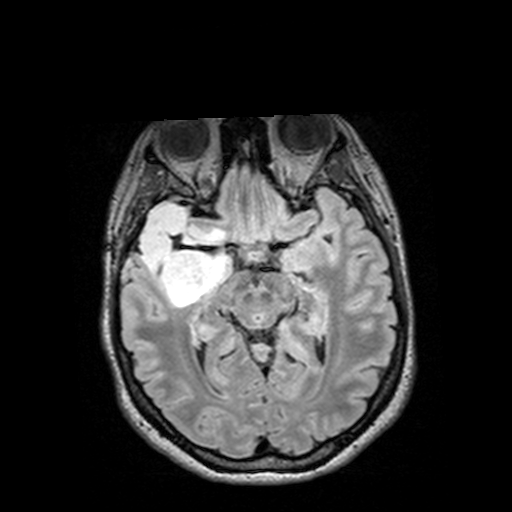
Brain MRI from a brain-tumour surgery series, one axial slice; position 83 of 144 along the scan axis; T2 FLAIR; 512 × 512 image matrix, field of view 250 × 250 mm. From the clinical record (not read from this slice): histopathology: Astrocytoma; WHO grade: 3; IDH mutation: yes; tumour location: Right Insular Temporal.
Structures marked on this image (expert manual segmentation):
- tumour: box from (x=126, y=202) to (x=232, y=307) px